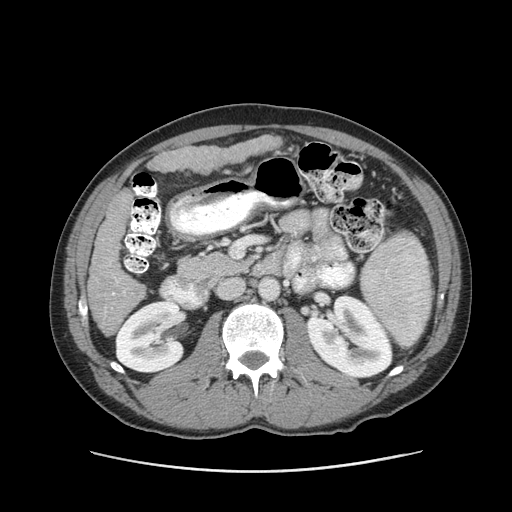
Contrast-enhanced abdominal CT (liver protocol), one axial slice; position 35 of 93 along the scan axis; reconstruction kernel STANDARD; soft-tissue window (W 400 / L 40 HU); 2.5 mm slice thickness; 512 × 512 image matrix. Case-level facts recorded for this patient, not image findings: diagnosis: hepatocellular carcinoma (patient treated with transarterial chemoembolisation; whether this scan precedes or follows treatment is not stated here); TNM stage (as recorded): Stage-II; Child-Pugh class: A; tumour differentiation: moderately differentiated; tumour nodularity: multinodular.
Annotated regions visible in this slice (semi-automatic segmentation, software-assisted and operator-edited):
- liver parenchyma outside the tumour (the mass and vessels are separate outlines, so this box may not span the whole liver): box from (x=88, y=135) to (x=282, y=336) px
- liver vessels: (x=112, y=280)–(x=117, y=296)